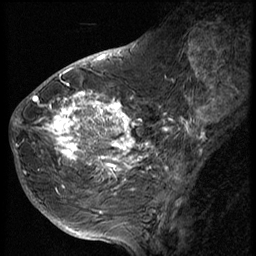
Breast MRI (dynamic contrast-enhanced), one sagittal slice; slice 23 of 56 in the series (ordered by position); 3 images stored at this slice position (order not interpretable as contrast timing); 1.5 T; TE 4.2 ms, TR 9 ms; 256 × 256 image matrix. Patient: female, 49 years. From the clinical record (not read from this slice): setting: breast cancer imaged before/during neoadjuvant chemotherapy; receptor status: HER2-positive.
Annotated regions visible in this slice (semi-automatically segmented with operator editing):
- analysis volume of interest (the breast-tissue region the enhancement analysis was run in; not a lesion): bounding box <37,85,143,207> (left, top, right, bottom; pixels)
- tumour enhancement mask (voxels above the 140 % enhancement threshold inside the analysis volume of interest): <37,85,143,182>